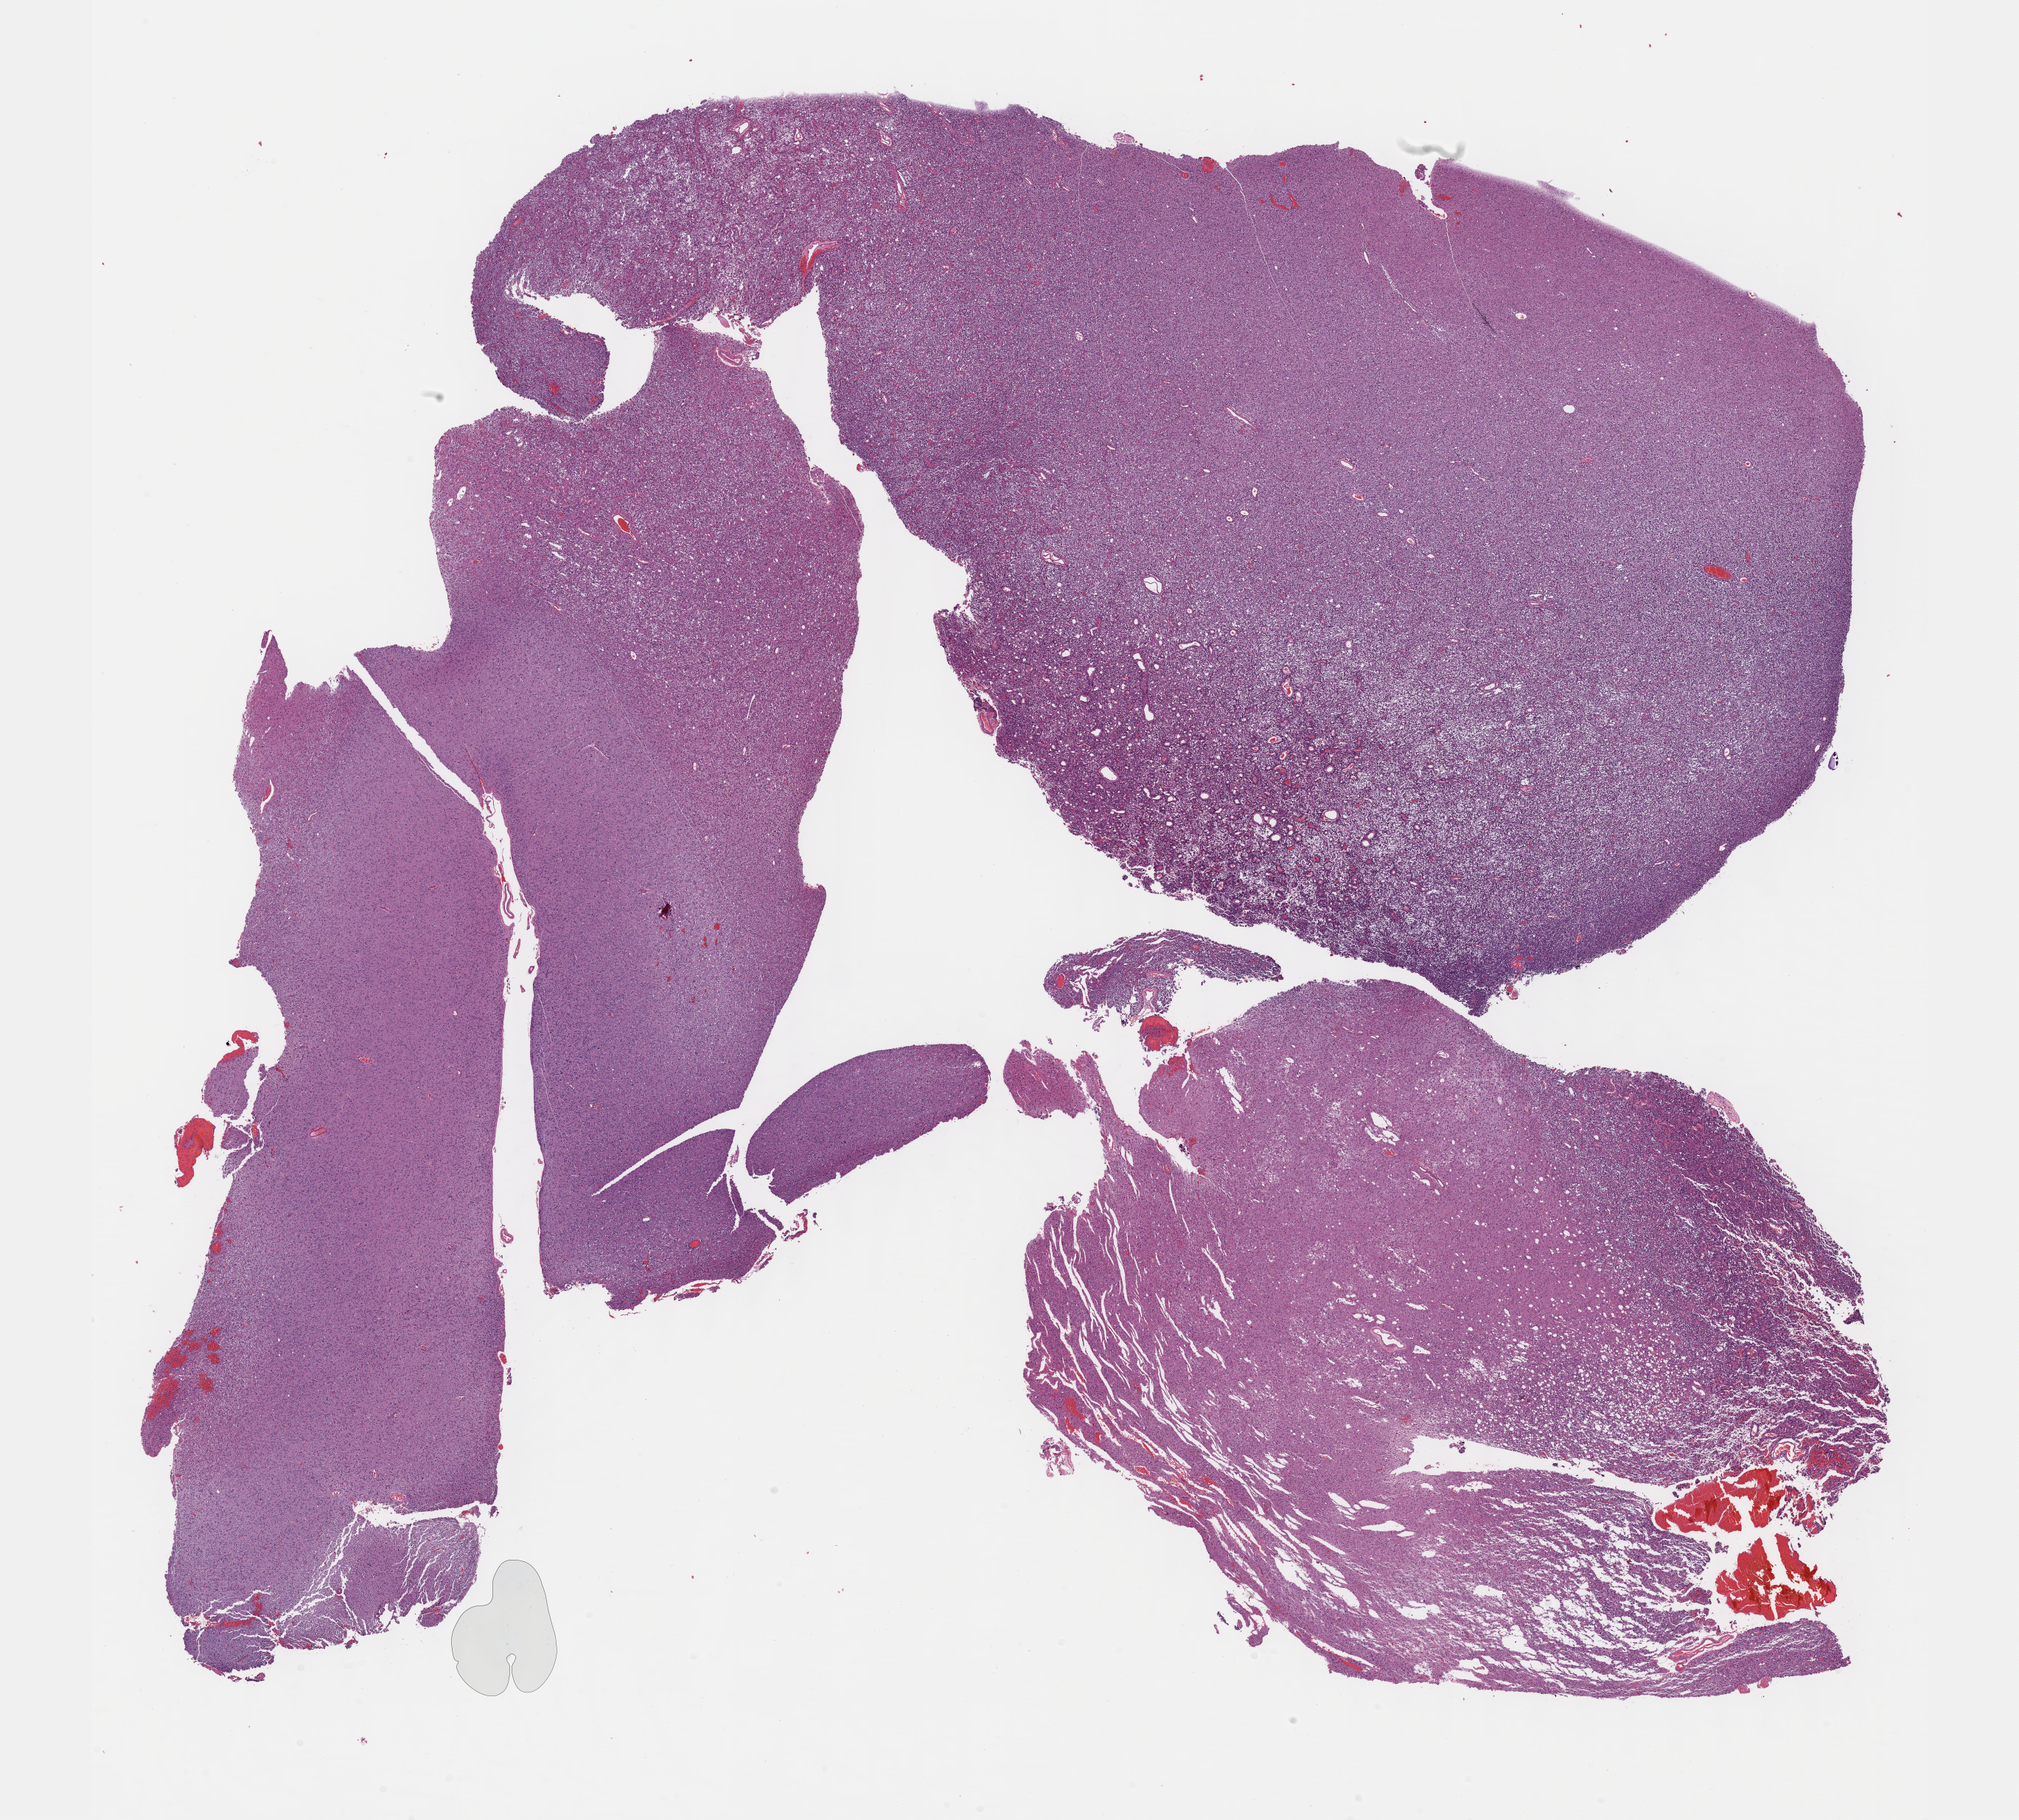
Digitized H&E tissue section (whole slide), shown as a low-resolution overview of the whole scanned area (about 22.1 x 19.9 mm, acquisition: 40x scan). Formalin-fixed paraffin-embedded (FFPE) diagnostic section. Primary tumour sample from the brain. Male patient; age at initial diagnosis 59 years. Histologic grade: G3 (poorly differentiated).
Pathologic diagnosis: Oligodendroglioma, anaplastic (cerebrum). Laterality: left.